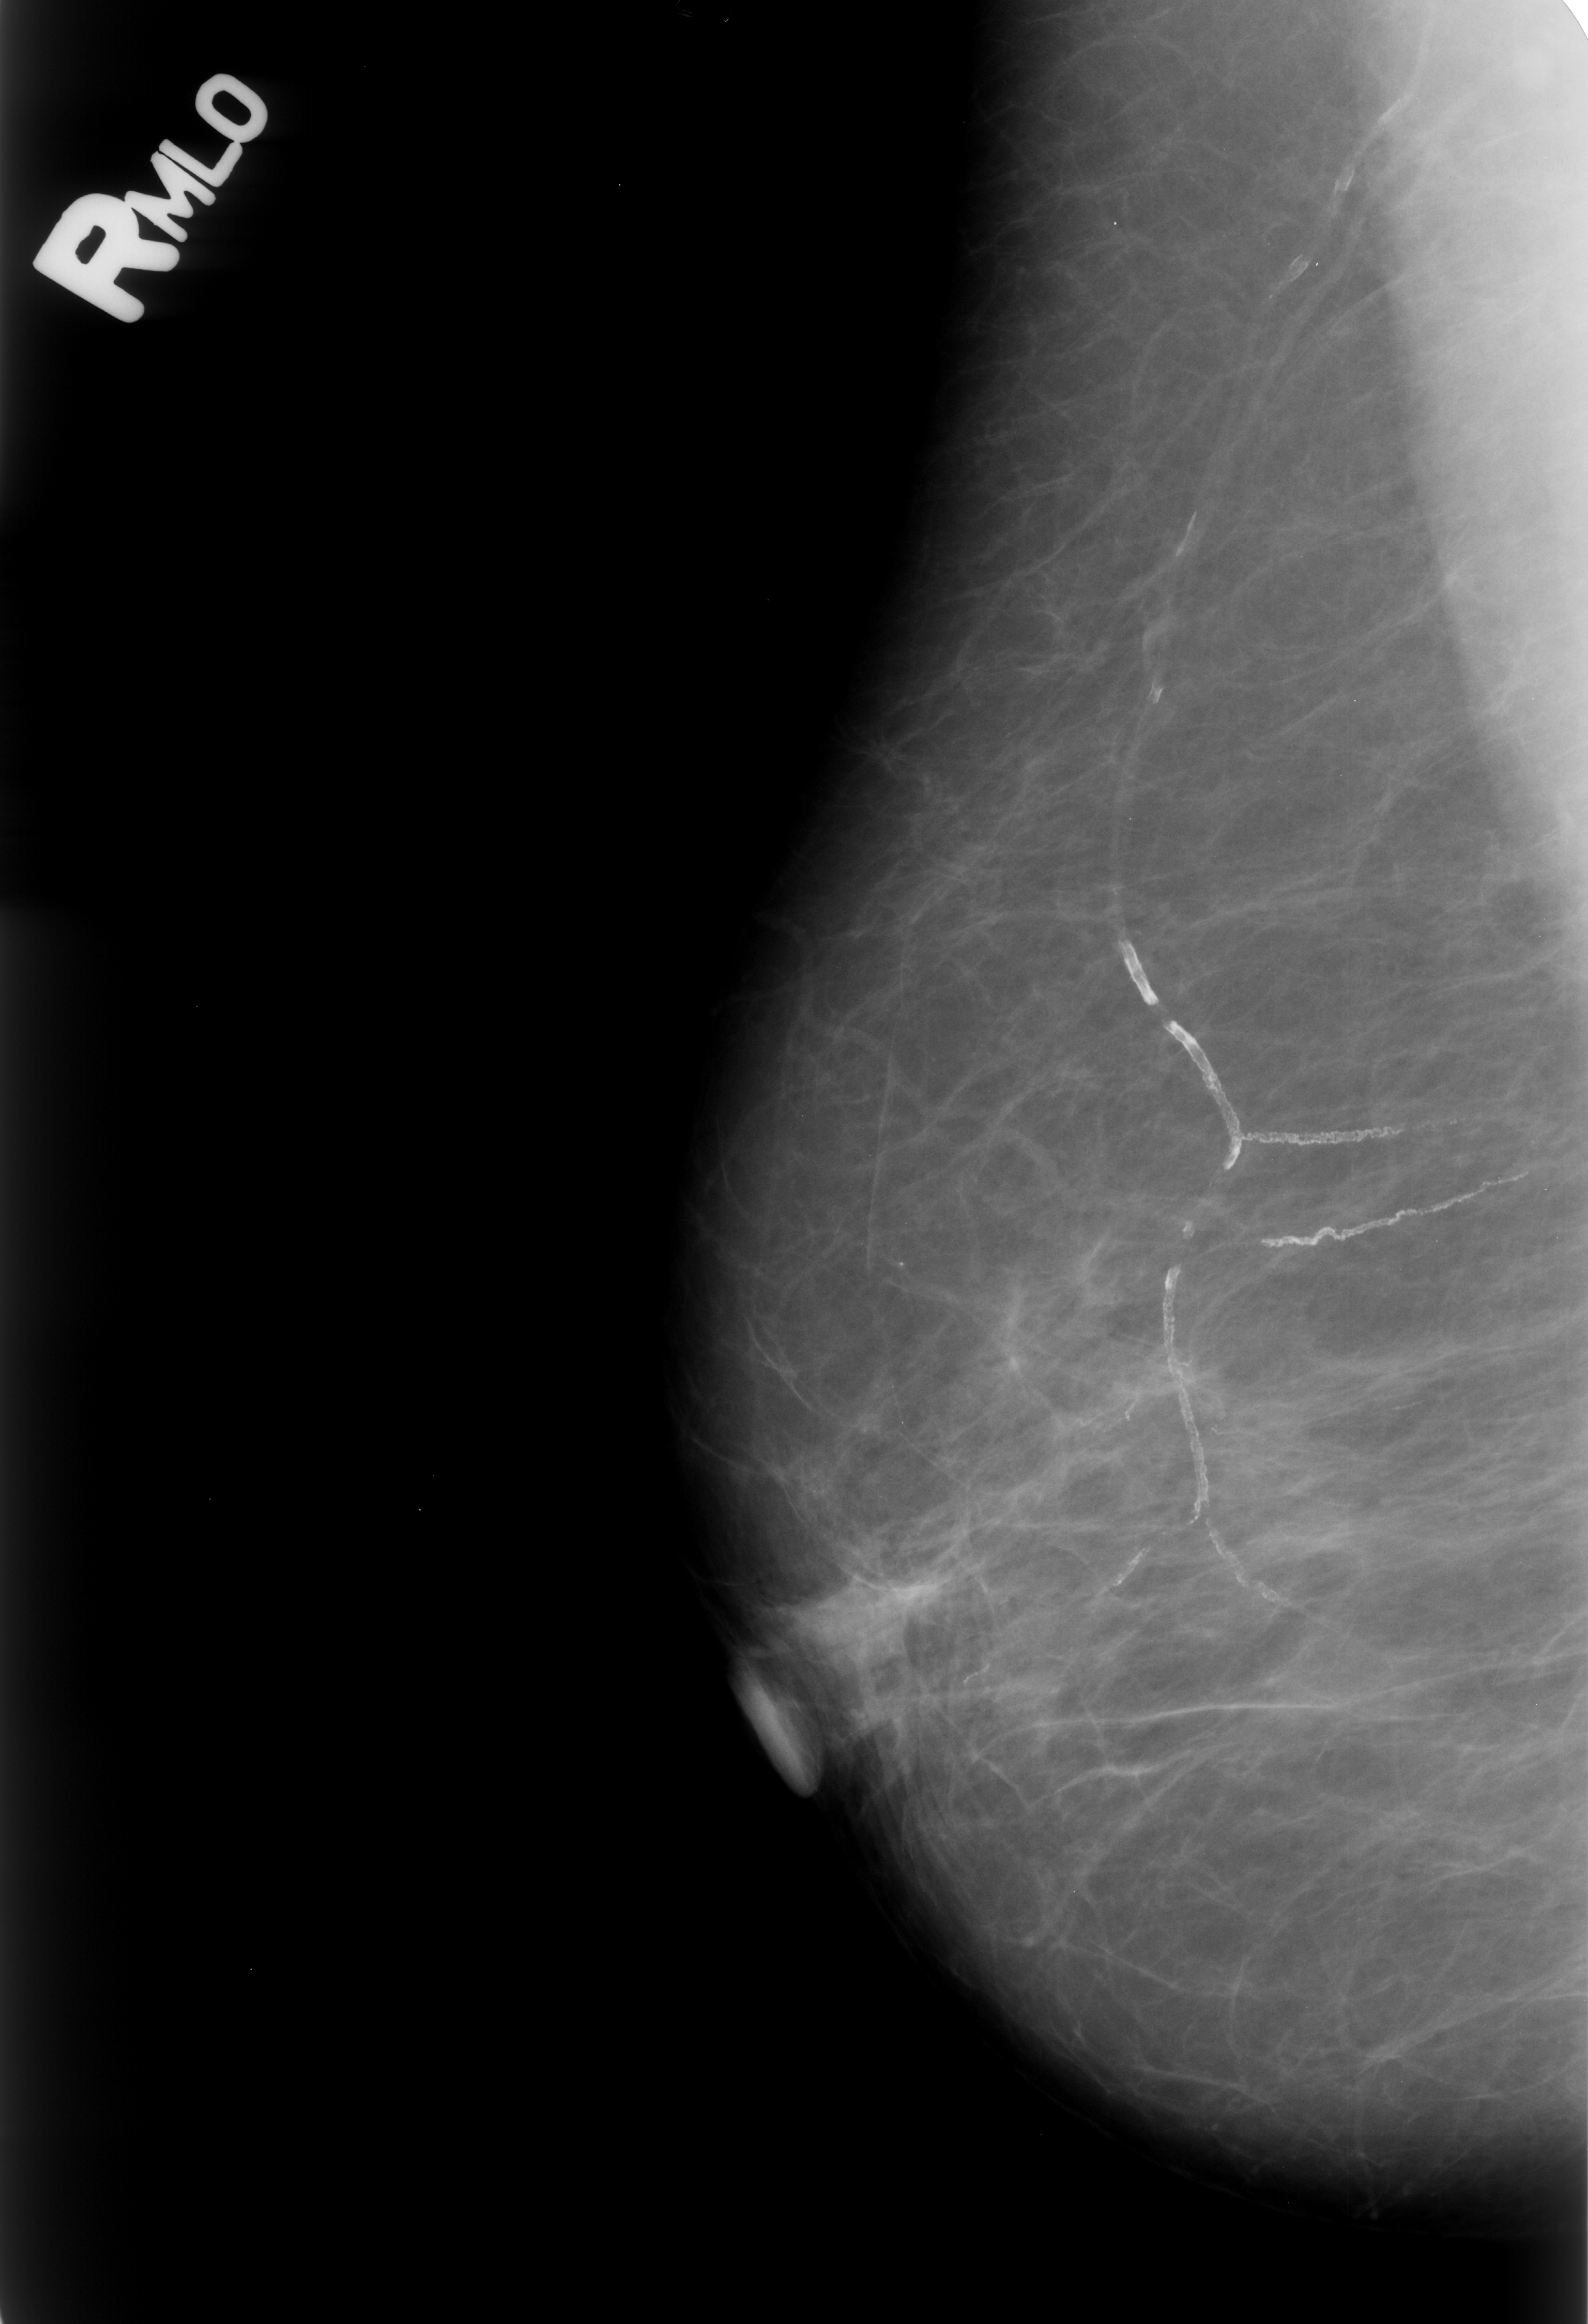
Scanned film-screen mammogram; right breast; MLO view; BI-RADS breast density category 1 (scale 1–4).
Abnormality record for this image: Finding 1 of 5: calcifications, morphology vascular; BI-RADS assessment category 2; subtlety rating 4 on a 1 (subtle) to 5 (obvious) scale; benign without callback (not worked up further). Finding 2 of 5: calcifications, morphology vascular; BI-RADS assessment category 2; benign; no additional work-up was recommended (benign without callback). Finding 3 of 5: calcifications, morphology vascular; BI-RADS assessment category 2; benign without callback (not worked up further). Finding 4 of 5: calcifications, morphology fine linear branching; BI-RADS assessment category 2; subtlety rating 4 on a 1 (subtle) to 5 (obvious) scale; benign without callback (not worked up further). Finding 5 of 5: calcifications, morphology fine linear branching; BI-RADS assessment category 2; subtlety rating 4 on a 1 (subtle) to 5 (obvious) scale; benign without callback (not worked up further).